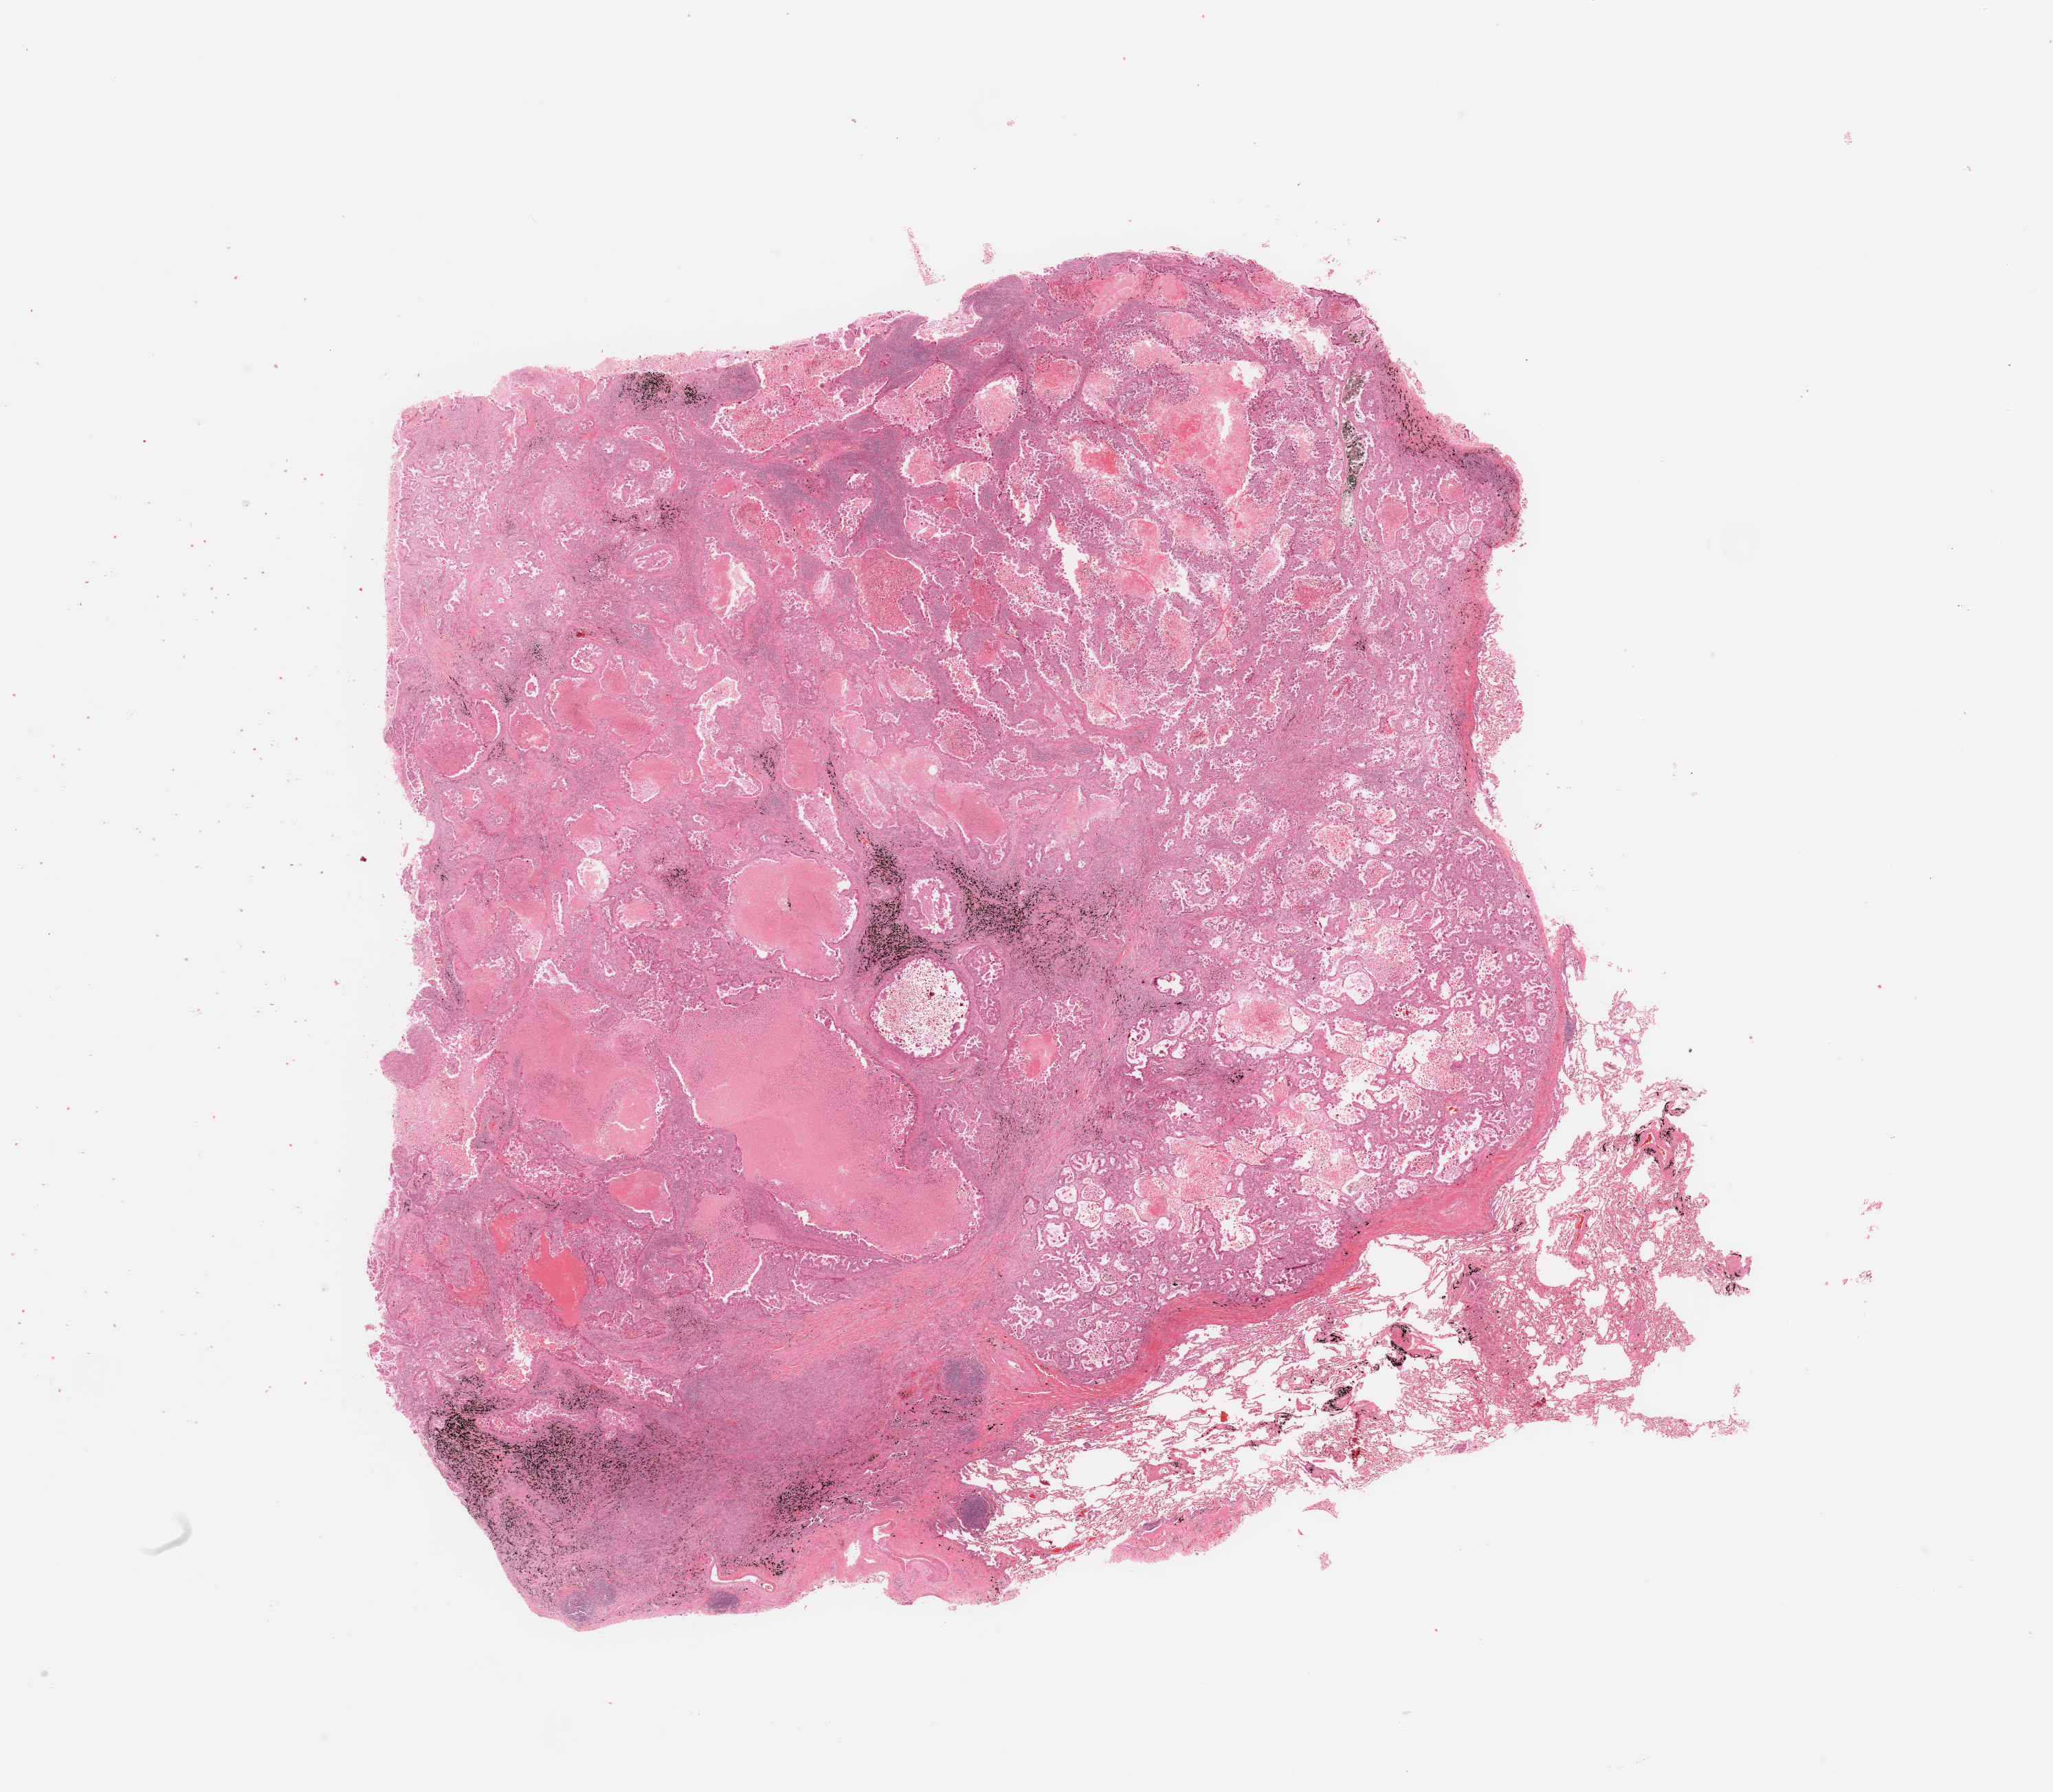
Whole-slide histology image, H&E, whole scanned area (about 23.6 x 20.6 mm, from a 20x scan) shown as a low-resolution overview. Lung, tumour tissue. 57-year-old male patient.
Histologic diagnosis: Adenocarcinoma, NOS.